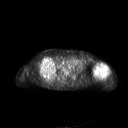
FDG PET of an extremity soft-tissue mass (from a PET/CT study), one axial slice; slice 147 of 267 in the series (ordered by position); 3.27 mm slice thickness; 128 × 128 image matrix. Patient: female, 83 years. From the clinical record (not read from this slice): histological type: pleiomorphic leiomyosarcoma; grade: high; site of the primary tumour: left biceps.
Outlined on this slice (expert contour drawn on MRI and transferred to this co-registered scan by the dataset authors):
- gross tumour volume including surrounding oedema: bounding box [x1, y1, x2, y2] px = [93, 63, 108, 77]
- gross tumour volume (mass): [93, 63, 108, 76]